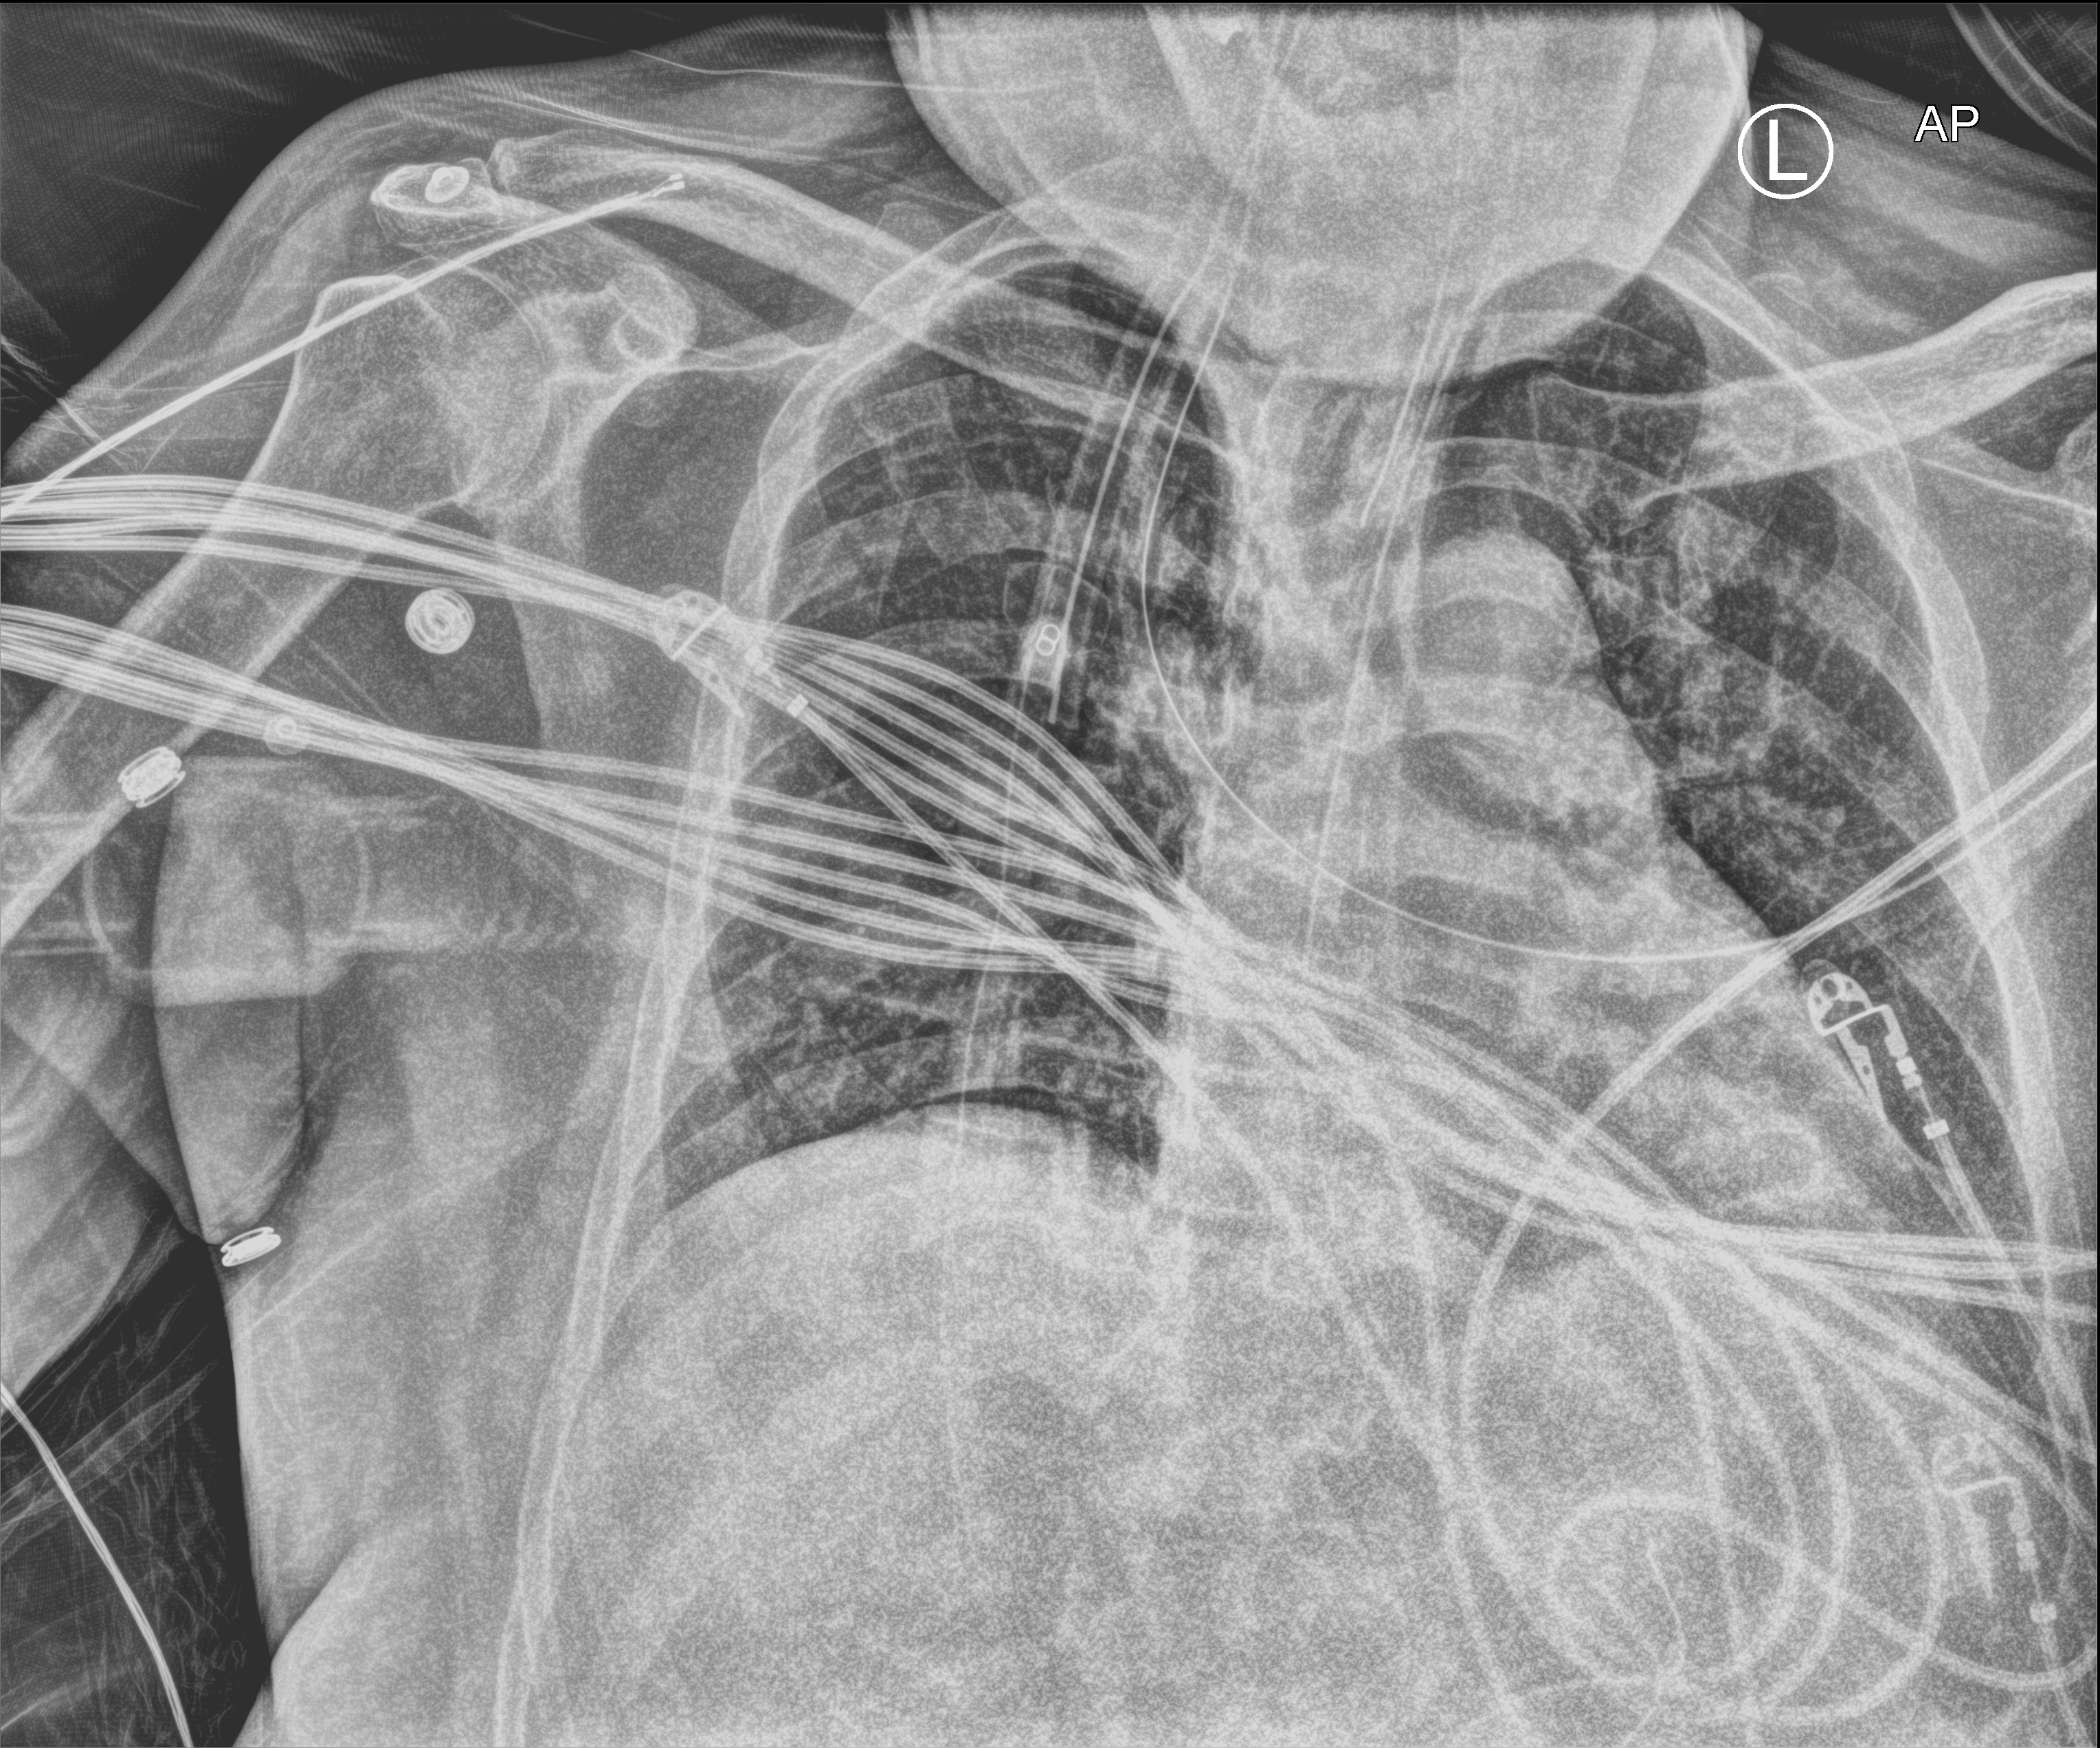
Chest X-ray (portable). Adult patient hospitalised with COVID-19, age 18–59 years.
Admission-level facts for this patient (not findings on this image; timing relative to this image not recorded):
- mechanically ventilated during this hospital stay: yes